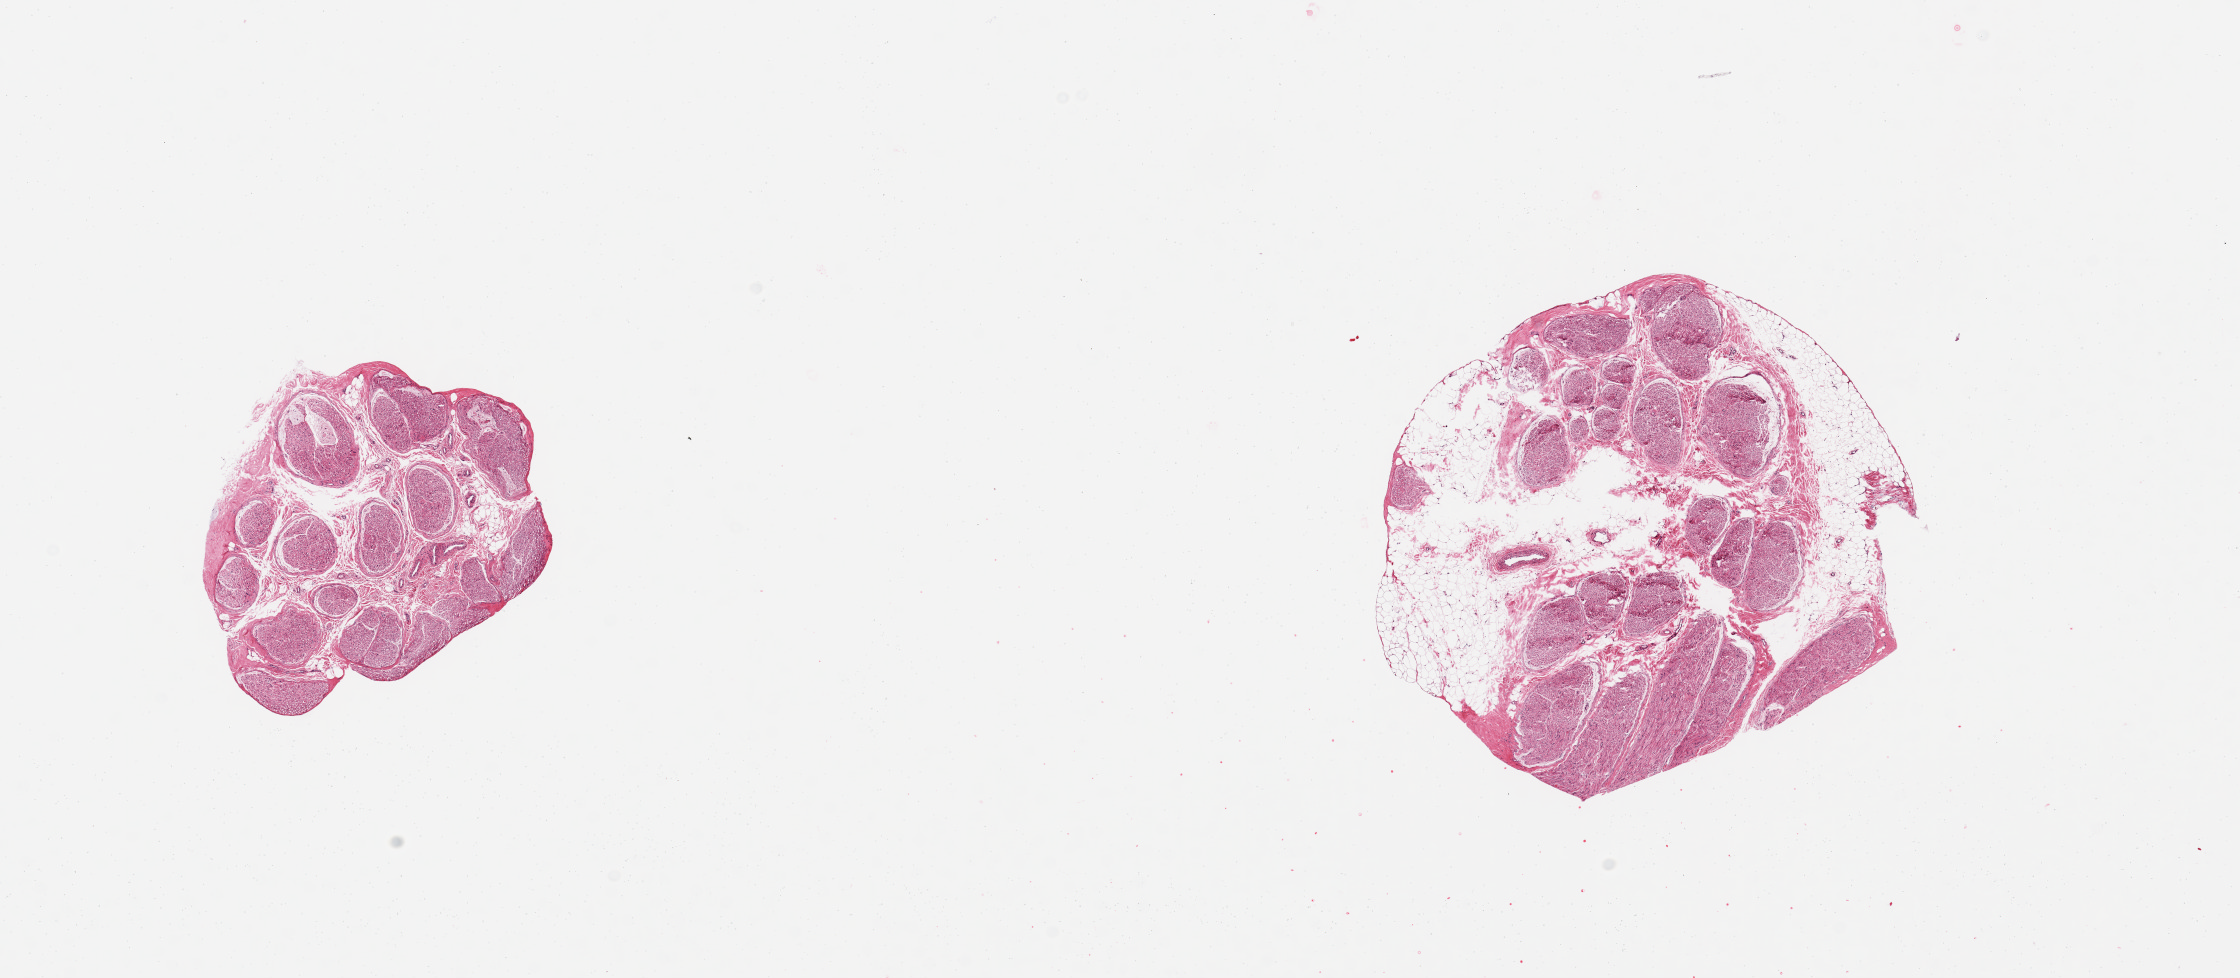
Hematoxylin and eosin (H&E) whole-slide image — a low-resolution overview of the entire scanned area, about 17.7 x 7.7 mm. PAXgene-fixed, paraffin-embedded tissue. Target tissue: tibial nerve. Donor tissue sample.
Review note (as recorded): 2 pieces; 1 piece includes ~30% attached fat.